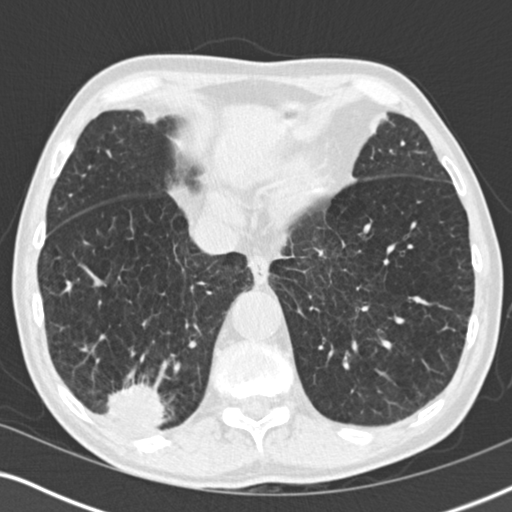
Low-dose screening chest CT, one axial slice; 120 kVp; lung window (W 1500 / L -600 HU); 2 mm slice thickness; 512 × 512 image matrix, field of view 330 × 330 mm.
Annotated regions visible in this slice (expert manual segmentation):
- lesion 3 (tumor, lower lobe of right lung): bounding box <105,381,165,428> (left, top, right, bottom; pixels)